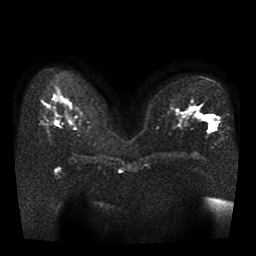
Breast MRI, one axial slice. Position 20 of 41 along the scan axis. Diffusion-weighted series; image 2 of 4 stored at this slice position (different b-values; order by instance number). 1.5 T. 256 × 256 image matrix, field of view 330 × 330 mm. Female patient.
Structures marked on this image (expert manual segmentation):
- tumour on diffusion-weighted imaging: bounding box (x1, y1, x2, y2) in pixels: (206, 116, 217, 128)